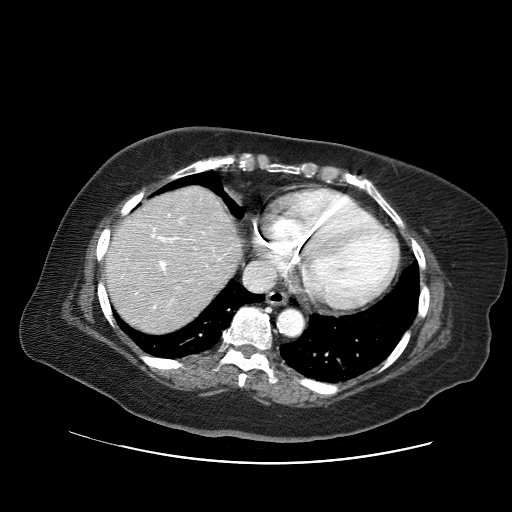
Contrast-enhanced abdominal CT (liver protocol), one axial slice; position 57 of 71 along the scan axis; reconstruction kernel STANDARD; 120 kVp; soft-tissue window (W 400 / L 40 HU); 2.5 mm slice thickness; 512 × 512 image matrix, field of view 400 × 400 mm. From the clinical record (not read from this slice): diagnosis: hepatocellular carcinoma (patient treated with transarterial chemoembolisation; whether this scan precedes or follows treatment is not stated here); TNM stage (as recorded): Stage-II.
Annotated regions visible in this slice (semi-automatically segmented with operator editing):
- liver parenchyma outside the tumour (the mass and vessels are separate outlines, so this box may not span the whole liver): bounding box <104,186,240,332> (left, top, right, bottom; pixels)
- liver vessels: <136,214,221,309>